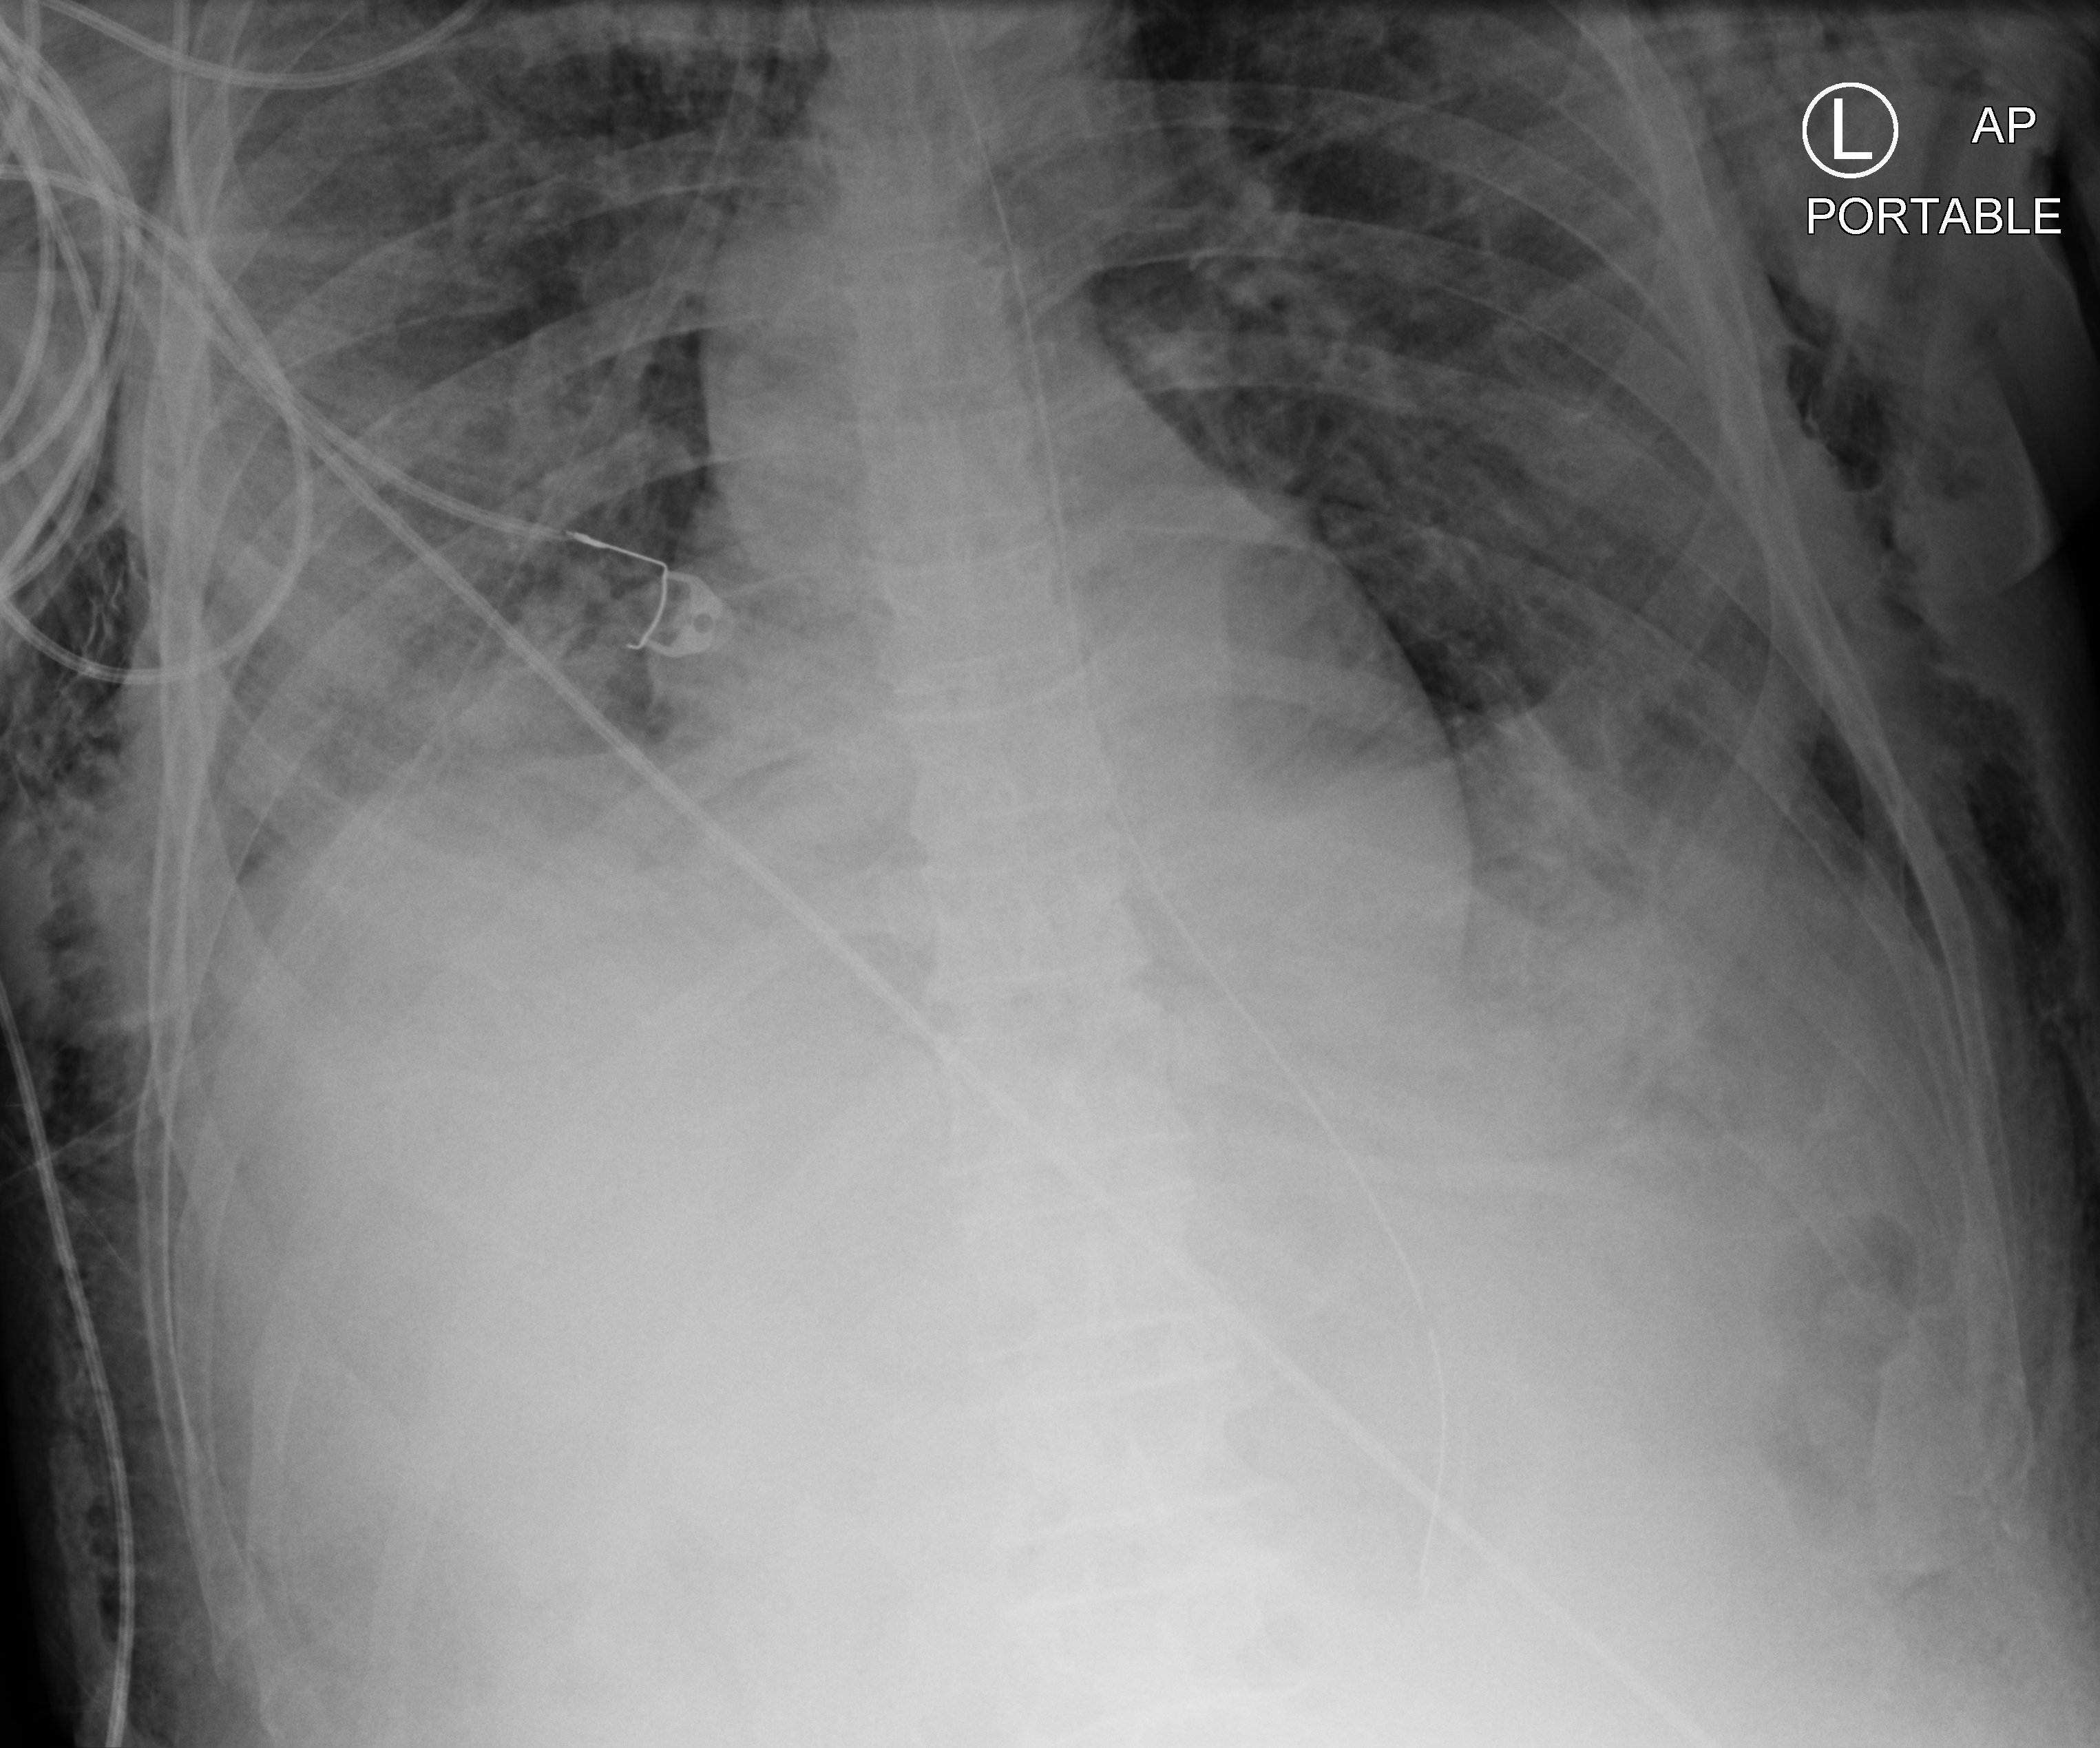
Portable chest radiograph. Male patient hospitalised with COVID-19, age 60–74 years.
Admission-level facts for this patient (not findings on this image; timing relative to this image not recorded):
- admitted to intensive care during this hospital stay: yes
- mechanically ventilated during this hospital stay: yes
- diabetes (admission record): no